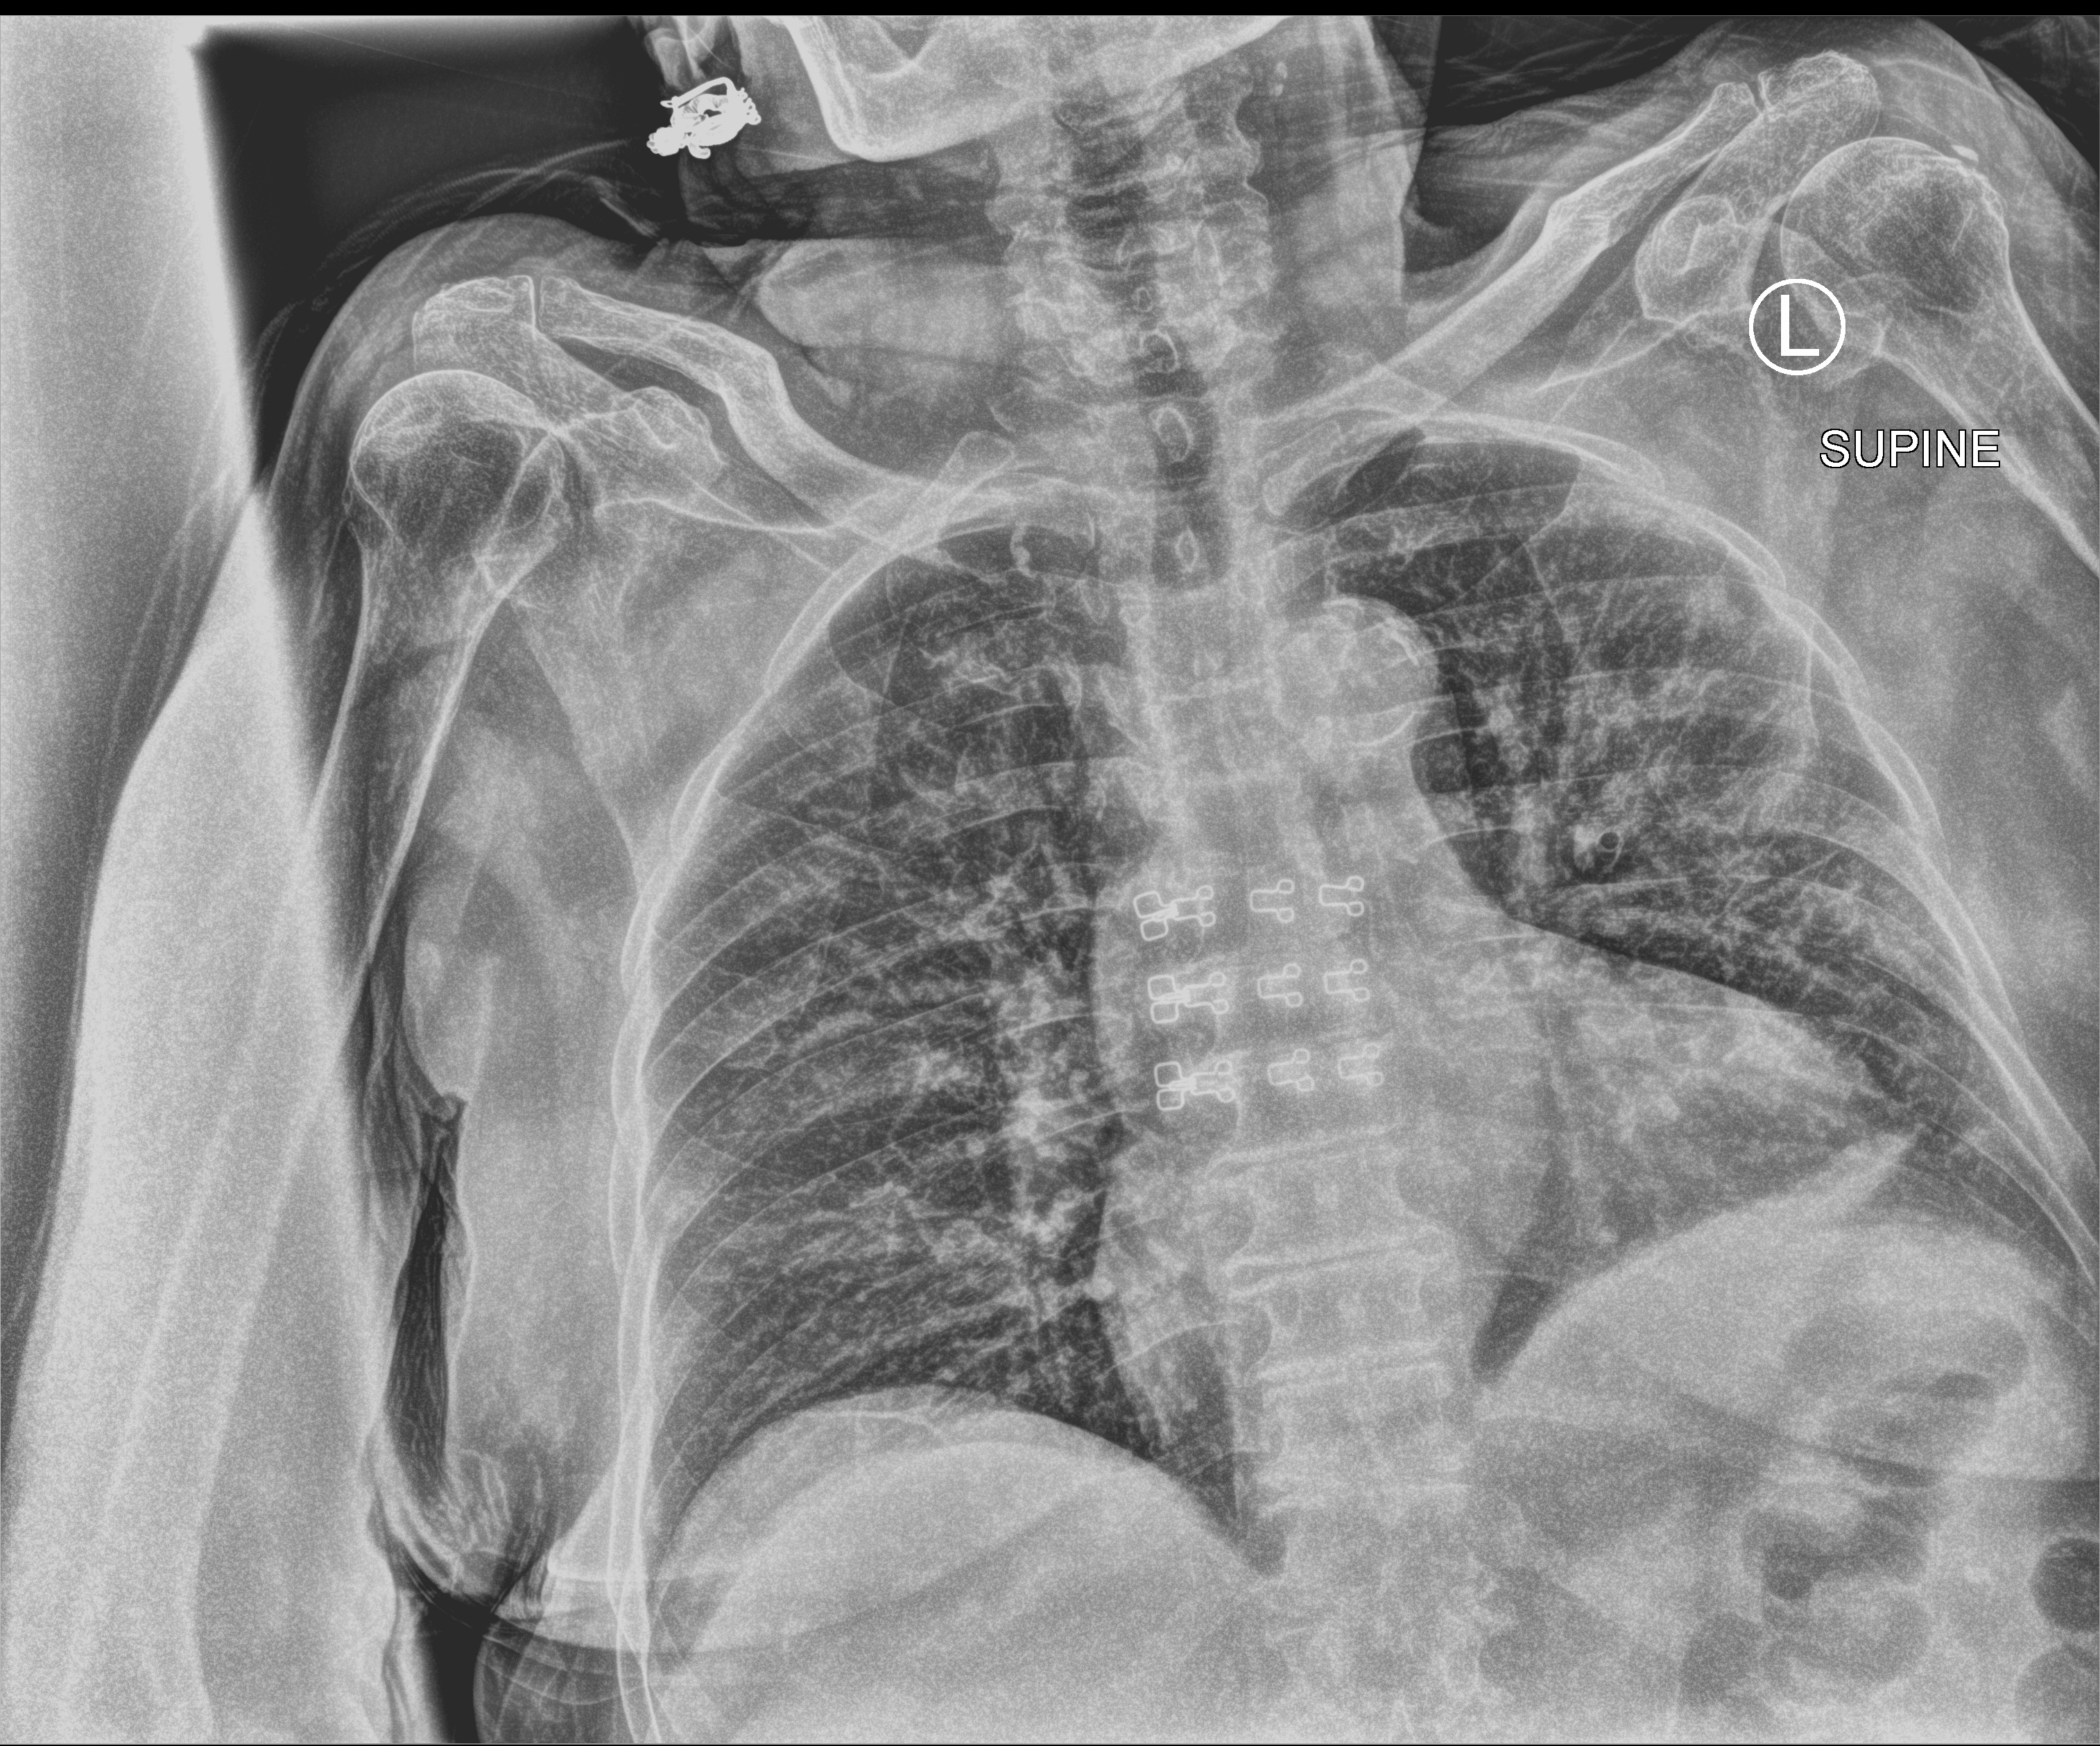
Portable chest radiograph. Female patient hospitalised with COVID-19, age 75–90 years.
From the hospital-stay record, not from the radiograph (when in the stay this image was taken is not recorded):
- admitted to intensive care during this hospital stay: no
- mechanically ventilated during this hospital stay: no
- hypertension (admission record): yes